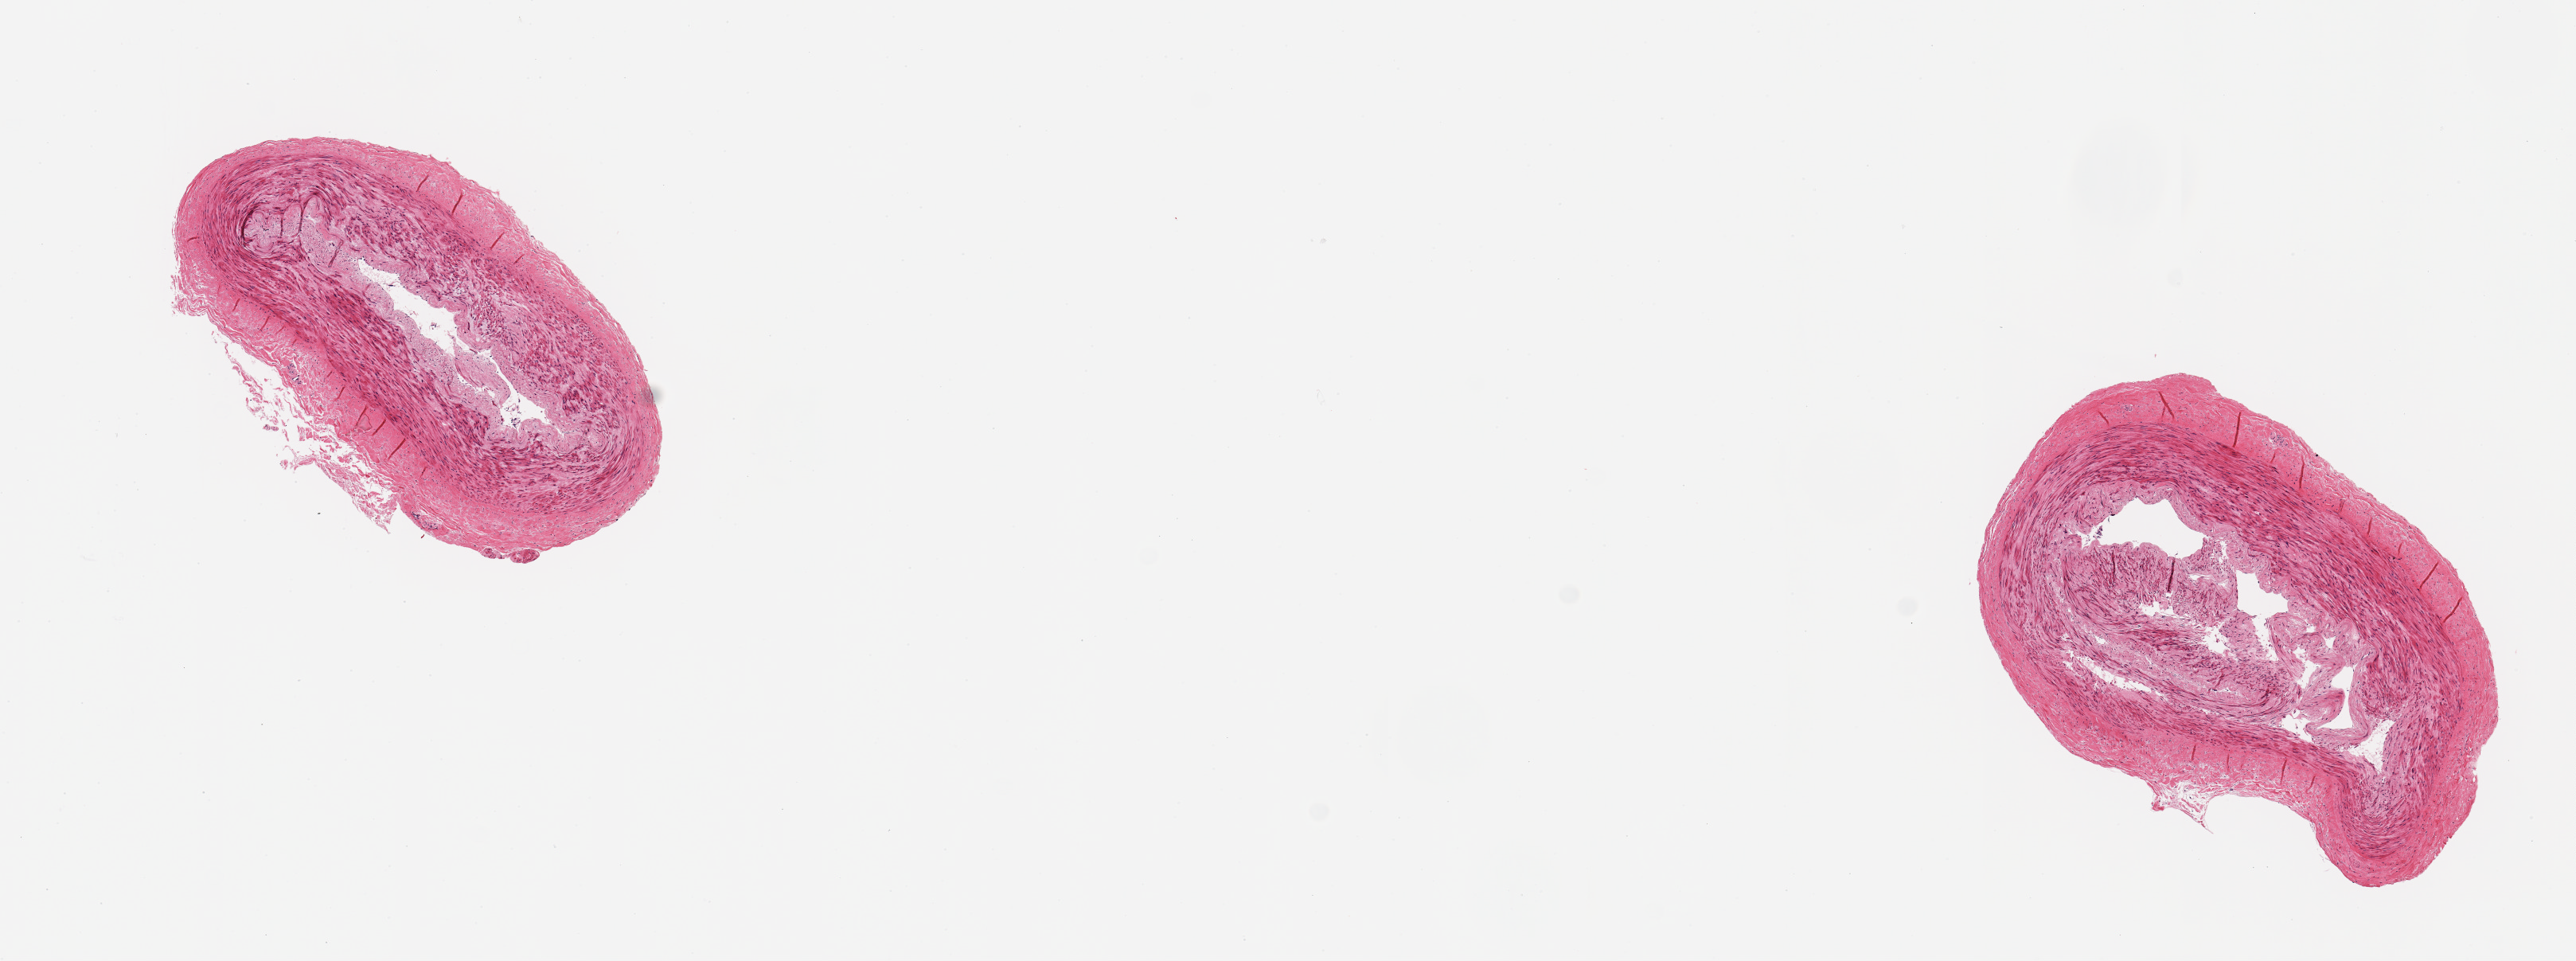
Digitized haematoxylin and eosin-stained section, brightfield — low-resolution overview of the scanned area, about 12.8 x 4.8 mm (from a 20x scan); PAXgene-fixed, paraffin-embedded tissue; section of tibial artery (target tissue); tissue donor sample. Male donor.
* reviewer comment on this tissue sample: 2 pieces, small muscular artery, minimal adherent fat/fascia; no atherosis